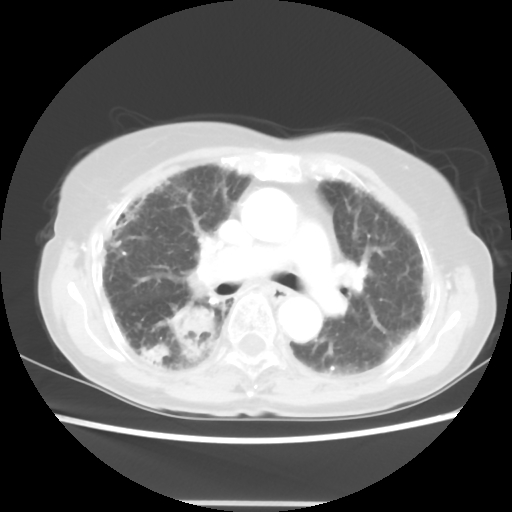
Chest CT, one axial slice. Slice 32 of 52 in the series (ordered by position). 120 kVp. Lung window (W 1500 / L -600 HU). 5 mm slice thickness. 512 × 512 image matrix, field of view 325 × 325 mm. Patient: female, 71 years. Case-level facts recorded for this patient, not image findings: clinical TNM (as recorded): T3 N0 M0.
Outlined on this slice (rectangle marked by the reading radiologist):
- lung tumour (recorded histology: squamous cell carcinoma): bounding box <168,302,216,365> (left, top, right, bottom; pixels)